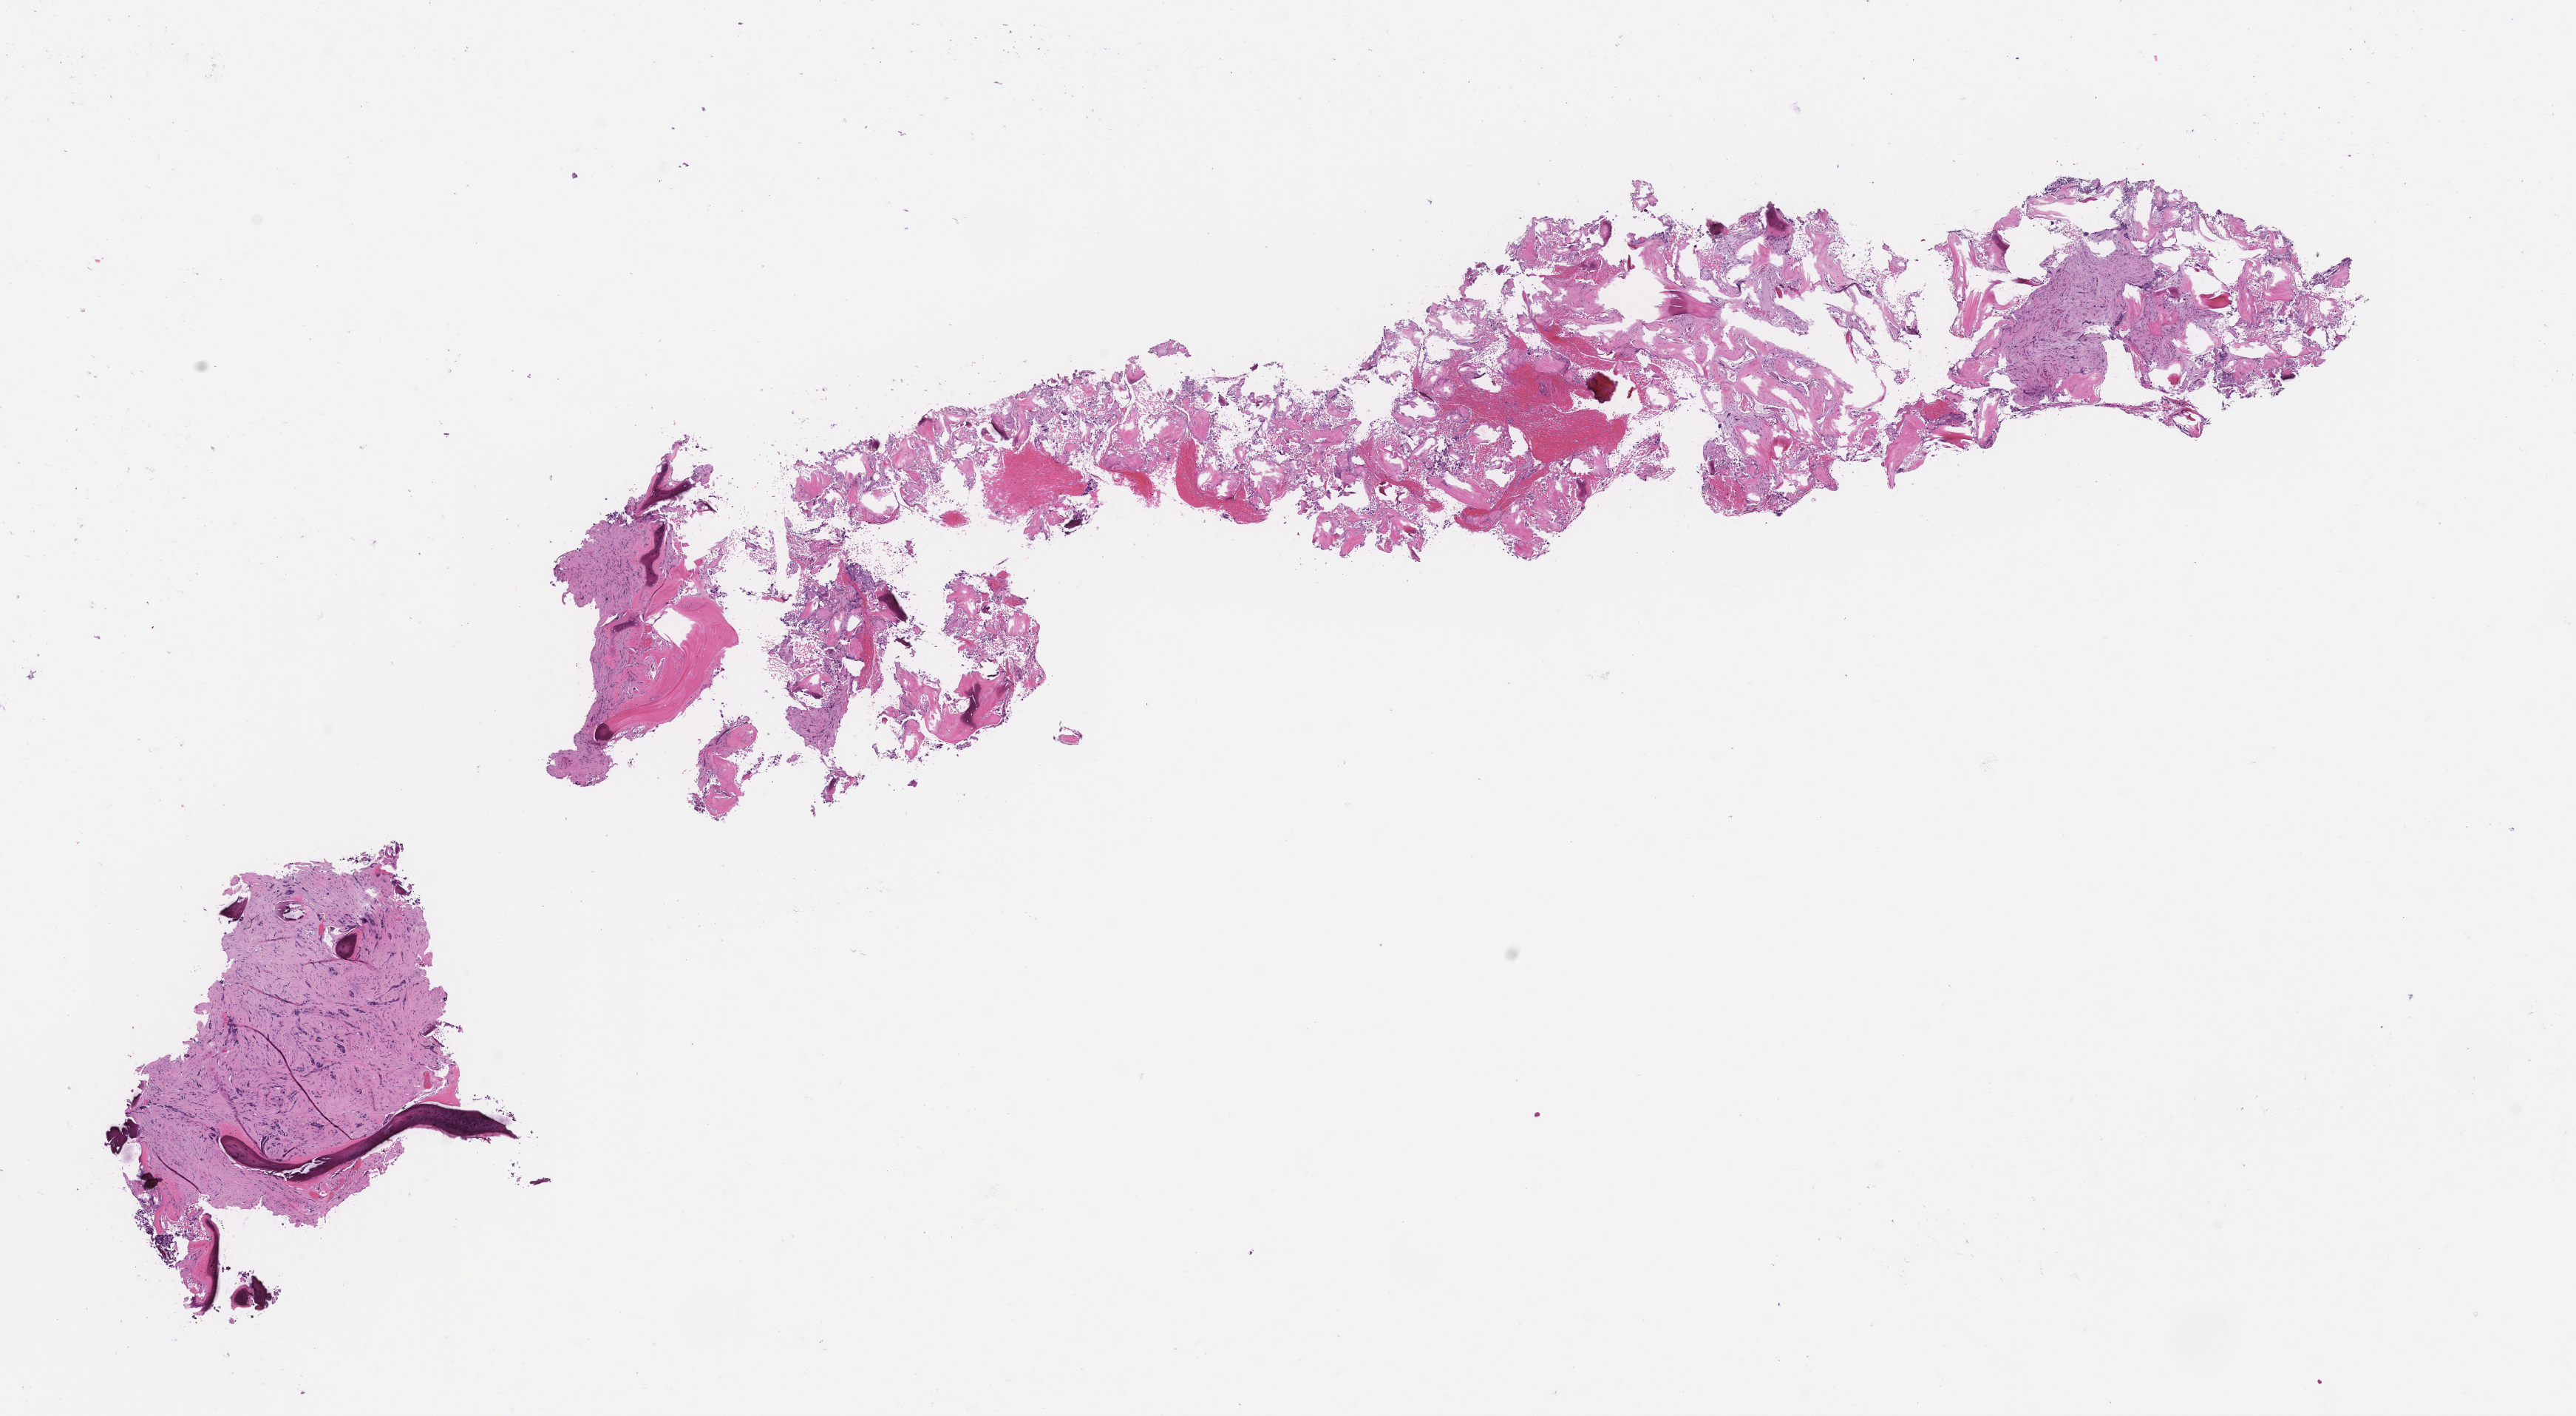
H&E whole-slide image — whole scanned area (about 14.1 x 7.7 mm) shown as a low-resolution overview. Formalin-fixed, paraffin-embedded (FFPE) tissue. Female patient.
- this section: metastasis (sampled organ not recorded)
- patient diagnosis (primary): Invasive Breast Carcinoma